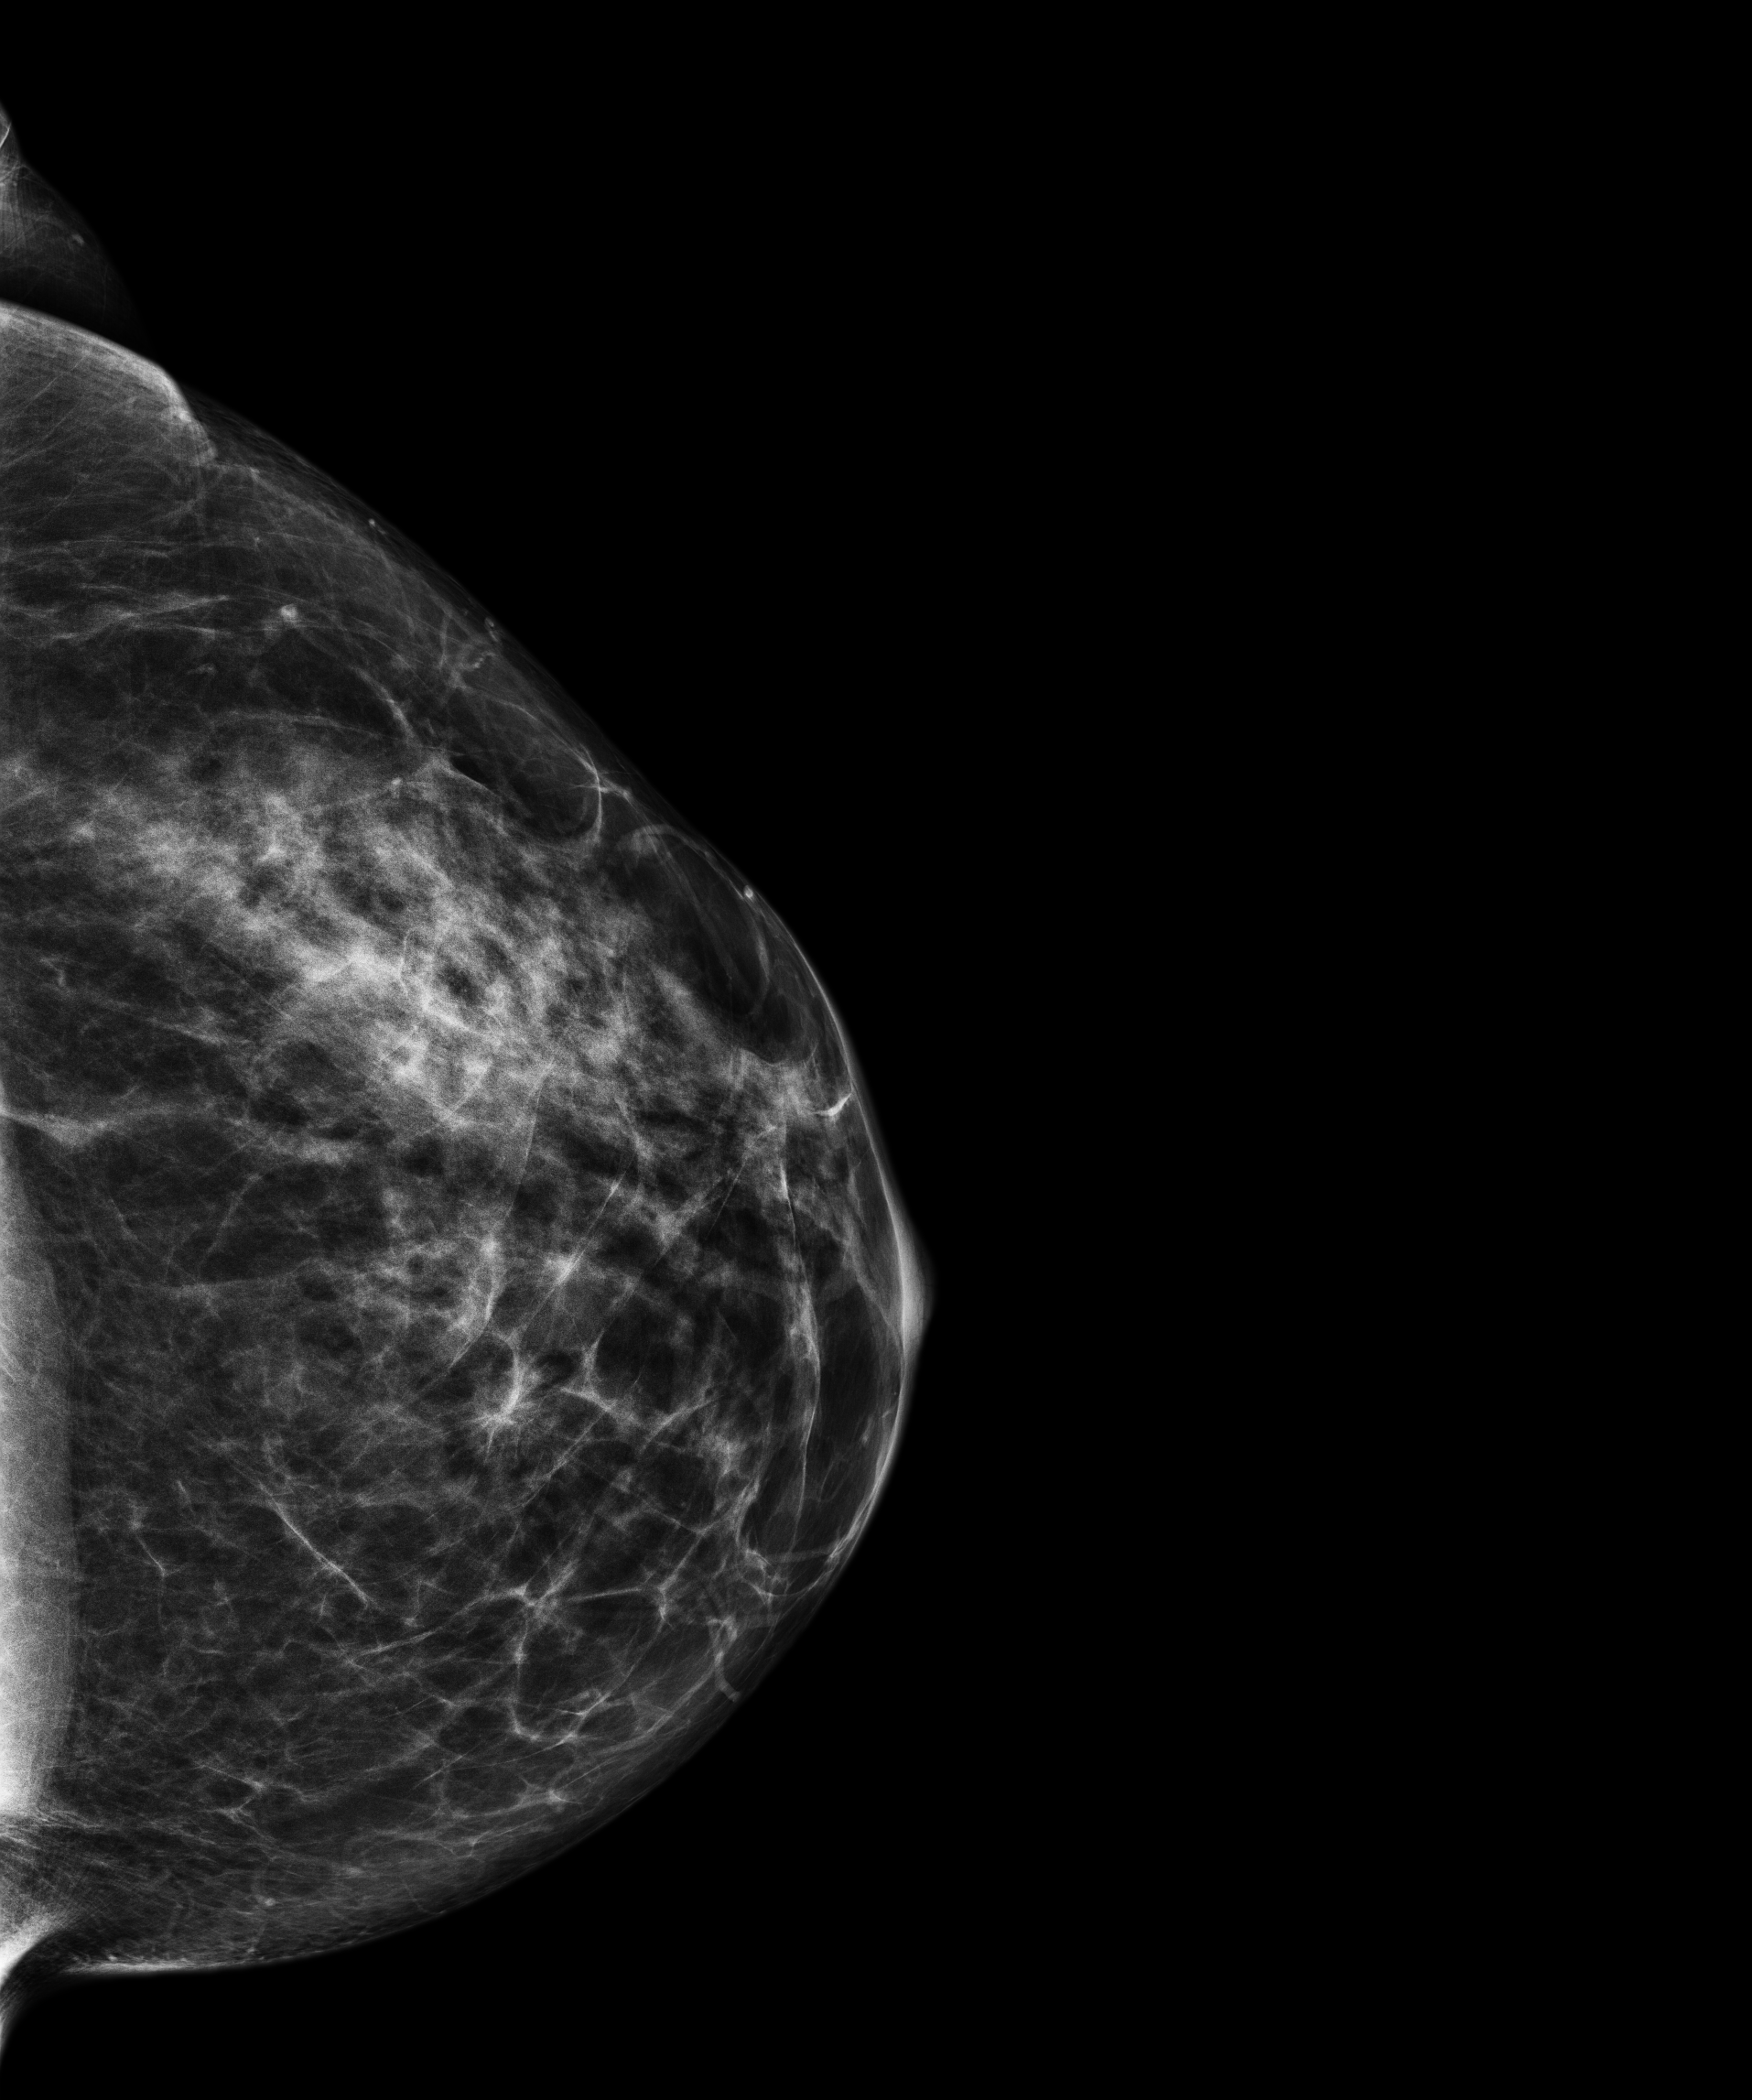
Annual screening mammography examination. Patient aged 46 years (female).
Image type: full-field digital mammogram. Breast: left. Projection: craniocaudal (CC) view.